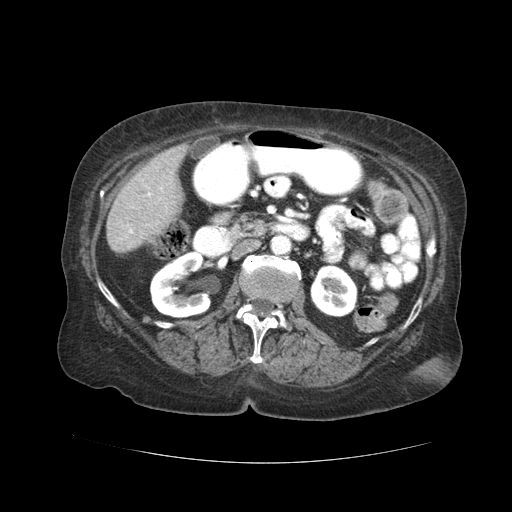
Contrast-enhanced abdominal CT (liver protocol), one axial slice; slice 4 of 59 in the series (ordered by position); reconstruction kernel STANDARD; 120 kVp; soft-tissue window (W 400 / L 40 HU); 2.5 mm slice thickness; 512 × 512 image matrix. From the clinical record (not read from this slice): diagnosis: hepatocellular carcinoma (patient treated with transarterial chemoembolisation; whether this scan precedes or follows treatment is not stated here); TNM stage (as recorded): Stage-I; Child-Pugh class: A; tumour nodularity: uninodular.
Structures marked on this image (semi-automatic segmentation, software-assisted and operator-edited):
- liver parenchyma outside the tumour (the mass and vessels are separate outlines, so this box may not span the whole liver): bounding box [x1, y1, x2, y2] px = [106, 144, 186, 252]
- liver vessels: [129, 193, 151, 233]